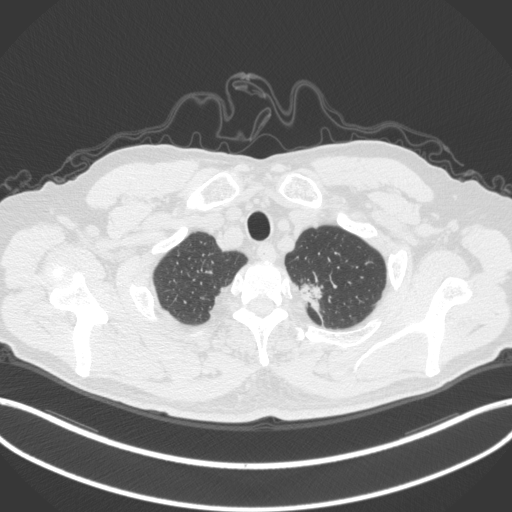
Chest CT, one axial slice. Slice 346 of 382 in the series (ordered by position). Reconstruction kernel B31f. 120 kVp. Lung window (W 1500 / L -600 HU). 1 mm slice thickness. 512 × 512 image matrix, field of view 400 × 400 mm. Patient: male, 64 years. Case-level facts recorded for this patient, not image findings: clinical TNM (as recorded): T1c N0 M0.
Structures marked on this image (bounding box drawn by a radiologist):
- lung tumour (recorded histology: adenocarcinoma): bounding box (x1, y1, x2, y2) in pixels: (299, 274, 328, 311)